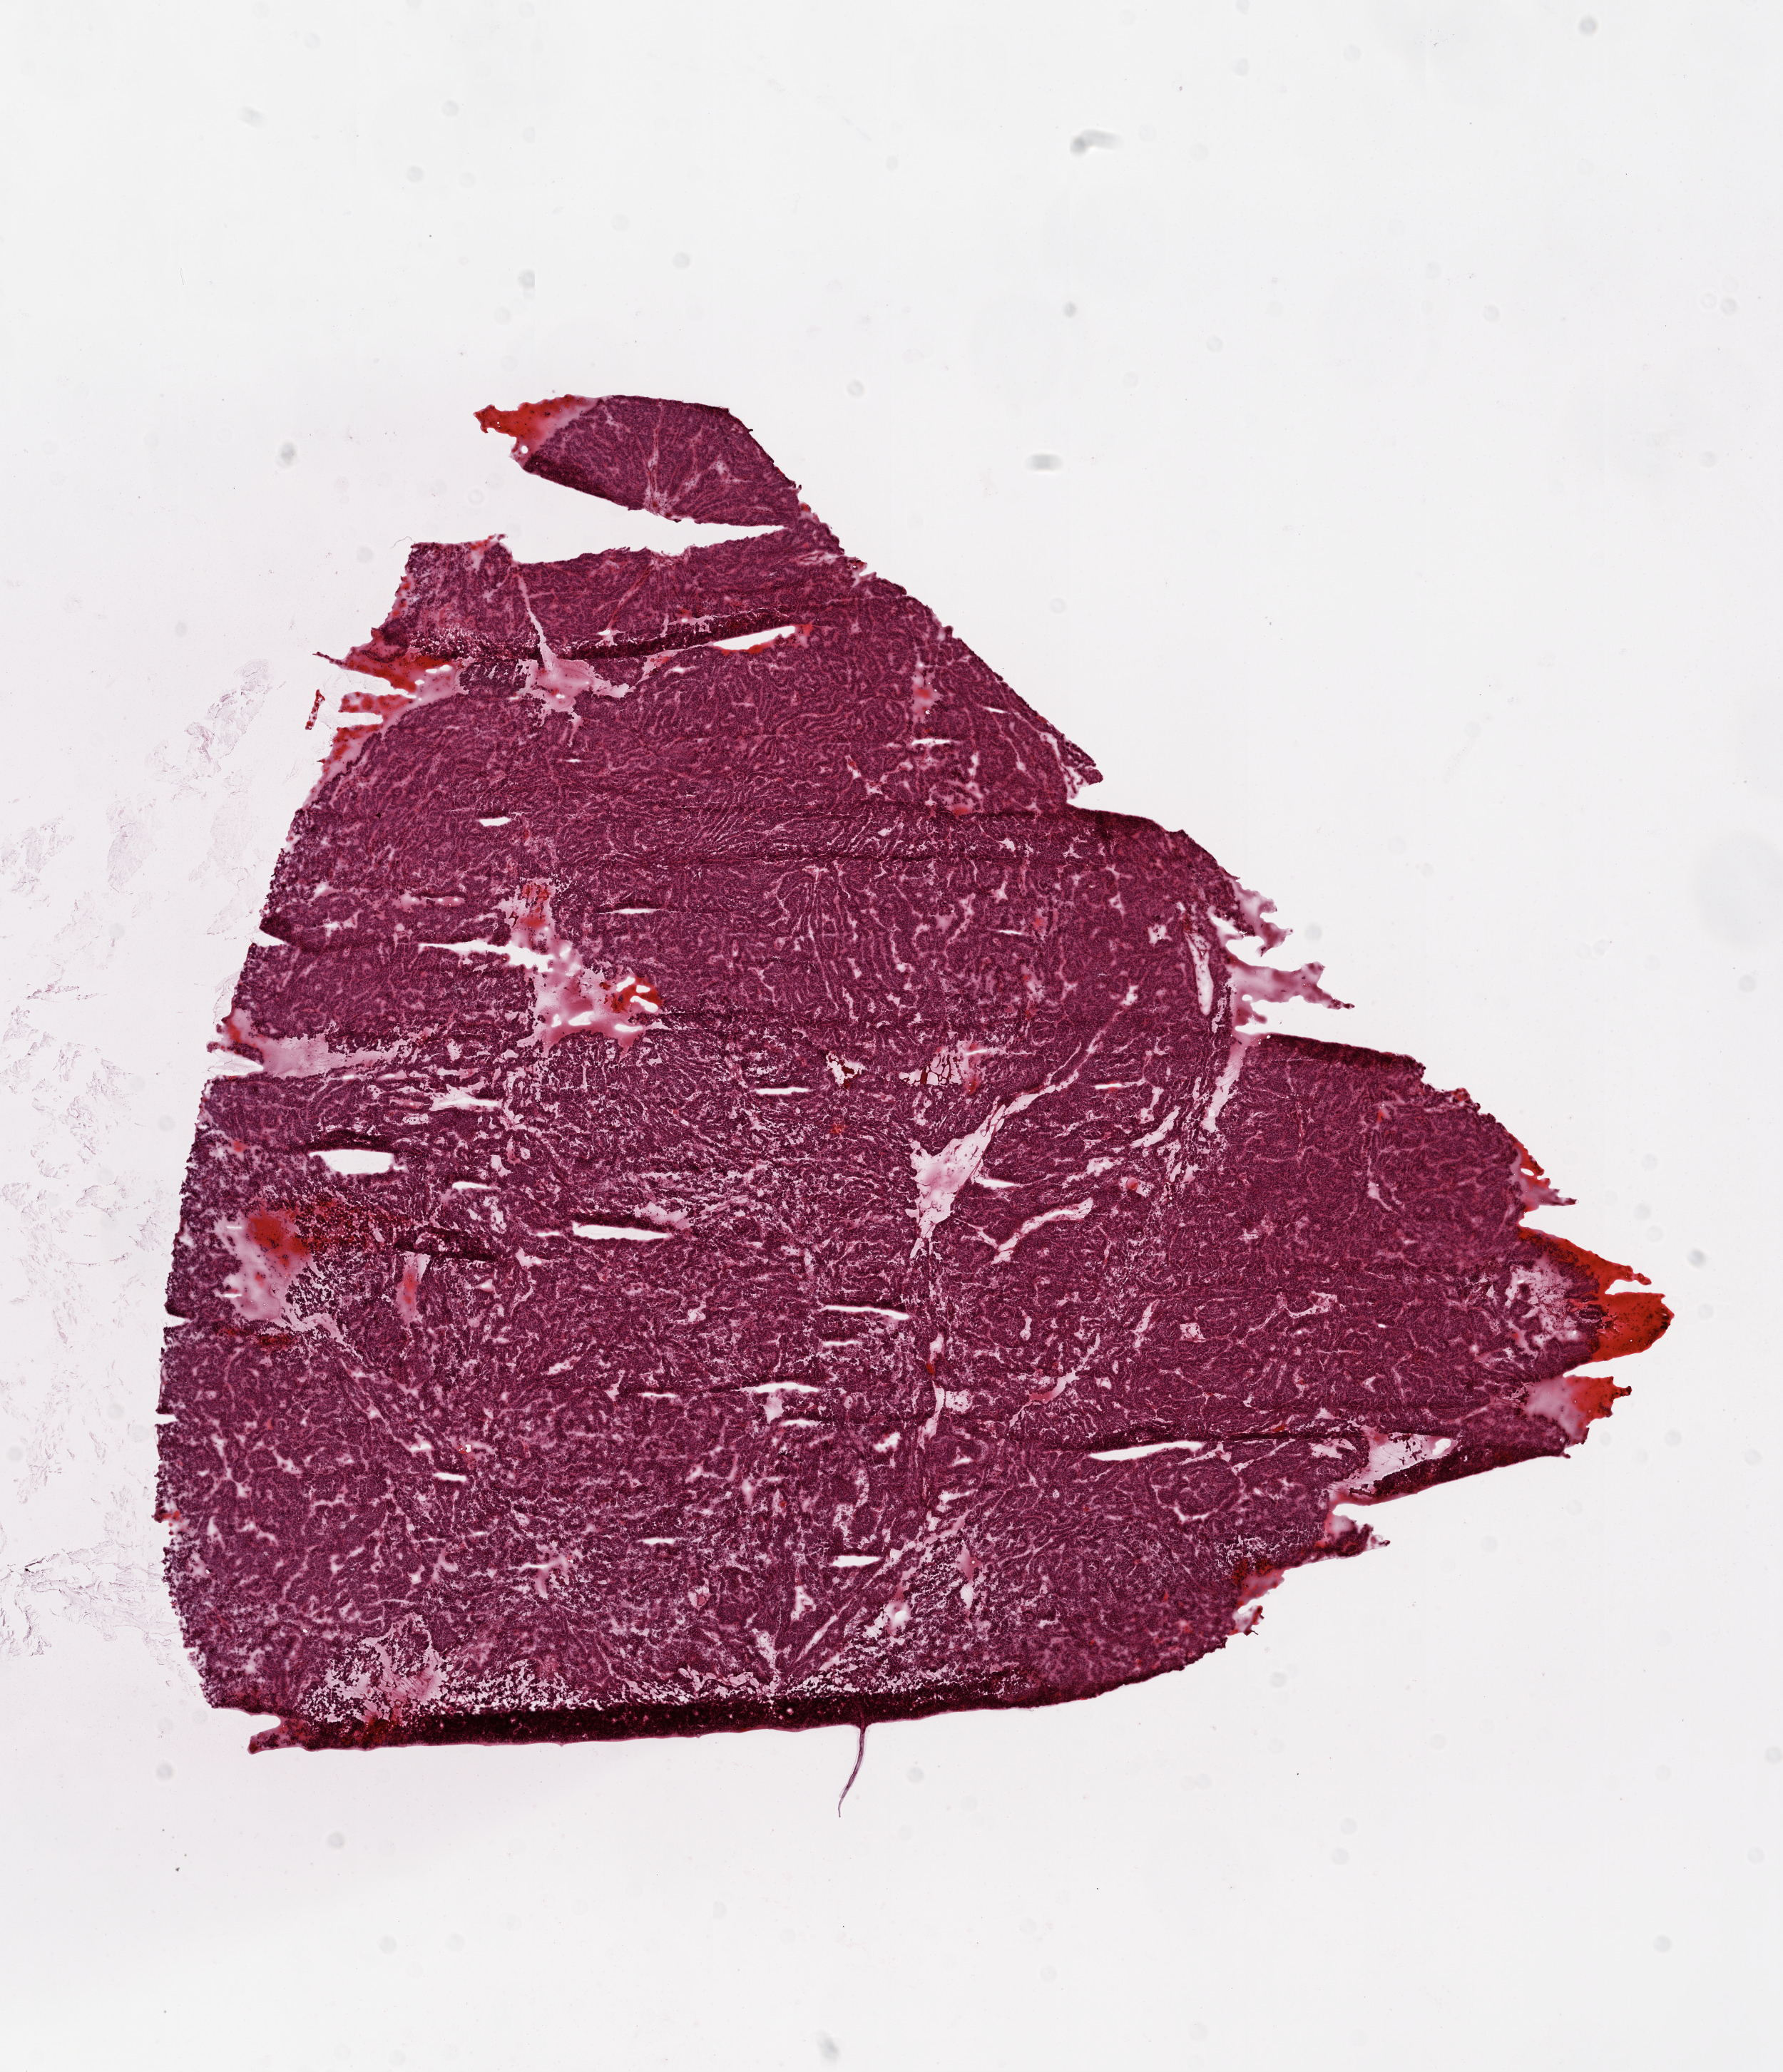
Whole-slide histology image, H&E-stained, a low-resolution overview of the entire scanned area, about 10.0 x 11.7 mm (slide scanned at 20x). Frozen section from the top of the tissue portion. Ovary, recurrent tumour sample. Female patient; age at initial diagnosis 55 years. Composition of this section per pathologist review: tumour cells 95%, tumour nuclei 99%, normal cells 0%, stromal cells 5%, necrosis 0%.
This section: recurrent tumour. Patient diagnosis: Serous surface papillary carcinoma.